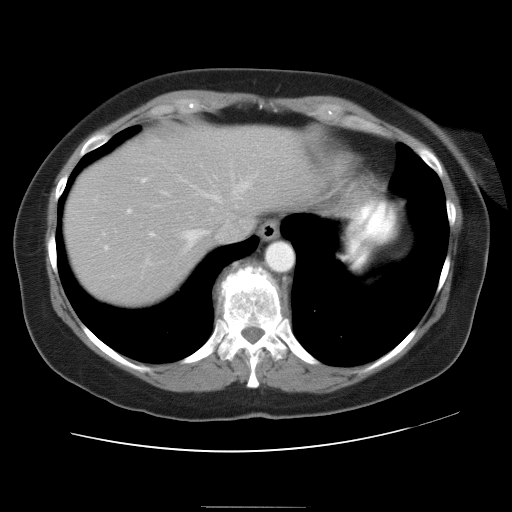
Contrast-enhanced abdominal CT, one axial slice; slice 27 of 30 in the series (ordered by position); 120 kVp; intravenous contrast given; soft-tissue window (W 400 / L 40 HU); 7.5 mm slice thickness; 512 × 512 image matrix, field of view 376 × 376 mm. Female patient, age 52 years. From the clinical record (not read from this slice): diagnosis: colorectal cancer liver metastases, imaged before liver resection; multiple liver metastases: no; largest metastasis: 3 cm; disease in both lobes: yes.
Outlined on this slice (manually delineated by an expert):
- hepatic veins: bounding box <187,185,245,247> (left, top, right, bottom; pixels)
- liver: <62,126,318,307>
- planned liver remnant (the part of the liver to remain after resection): <172,126,317,215>
- portal vein (with intrahepatic branches): <127,179,145,213>